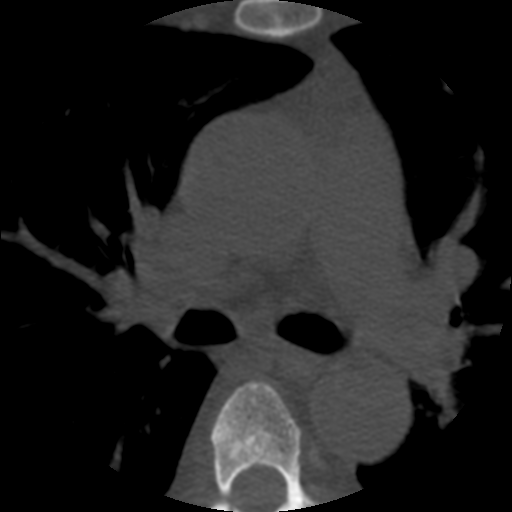
CT including the spine, one axial slice. Position 376 of 508 along the scan axis. Reconstruction kernel STANDARD. Bone window (W 1800 / L 400 HU). 1.25 mm slice thickness. 512 × 512 image matrix. Patient age 57 years. From the clinical record (not read from this slice): primary cancer: prostate.
Outlined on this slice (semi-automatic segmentation, software-assisted and operator-edited):
- T5 vertebra: box from (x=211, y=381) to (x=318, y=512) px
- T6 vertebra: (x=211, y=504)–(x=215, y=506)